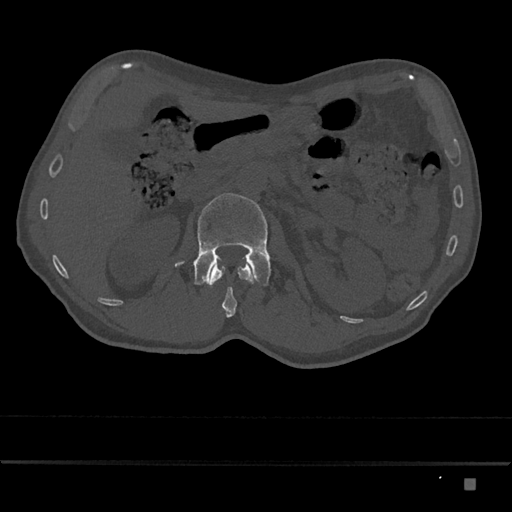
CT including the spine, one axial slice; position 501 of 797 along the scan axis; reconstruction kernel Br40s/3; bone window (W 1800 / L 400 HU); 0.5 mm slice thickness; 512 × 512 image matrix, field of view 390 × 390 mm. Male patient, age 72 years. Case-level facts recorded for this patient, not image findings: primary cancer: prostate.
Outlined on this slice (semi-automatically segmented with operator editing):
- L1 vertebra: box from (x=207, y=258) to (x=255, y=318) px
- L2 vertebra: (x=174, y=193)–(x=271, y=287)